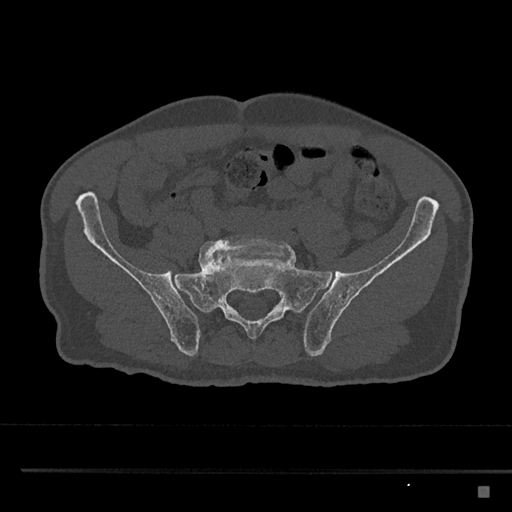
CT including the spine, one axial slice; slice 537 of 797 in the series (ordered by position); 120 kVp; bone window (W 1800 / L 400 HU); 0.5 mm slice thickness; 512 × 512 image matrix, field of view 391 × 391 mm. Patient: male, 59 years. Case-level facts recorded for this patient, not image findings: primary cancer: prostate.
Annotated regions visible in this slice (semi-automatically segmented with operator editing):
- L5 vertebra: bounding box (x1, y1, x2, y2) in pixels: (199, 235, 291, 271)